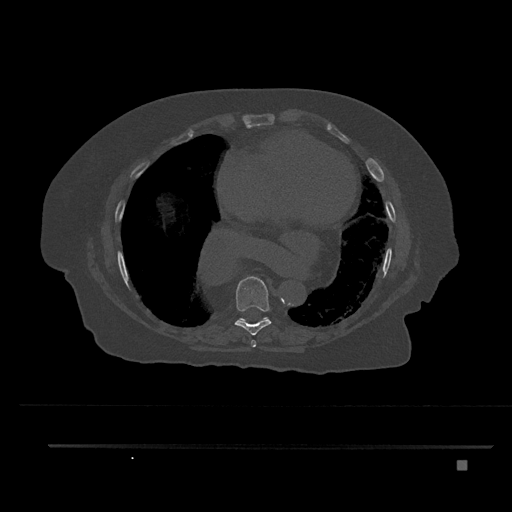
CT including the spine, one axial slice. Slice 436 of 797 in the series (ordered by position). Reconstruction kernel Br40s/3. 120 kVp. Bone window (W 1800 / L 400 HU). 0.5 mm slice thickness. 512 × 512 image matrix, field of view 437 × 437 mm. Patient: female, 76 years. From the clinical record (not read from this slice): primary cancer: lung; vertebrae with lytic lesions (as recorded): T11, L3.
Structures marked on this image (semi-automatic segmentation, software-assisted and operator-edited):
- T7 vertebra: box from (x=251, y=340) to (x=256, y=347) px
- T8 vertebra: (x=234, y=276)–(x=272, y=335)
- T9 vertebra: (x=239, y=318)–(x=246, y=322)